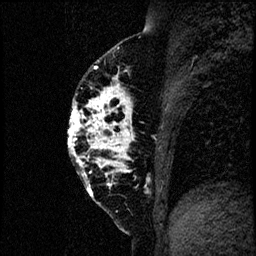
Breast MRI (dynamic contrast-enhanced), one sagittal slice. Slice 33 of 60 in the series (ordered by position). Dynamic contrast-enhanced study with each time point stored as its own series, time point 2 of 4 at this slice position (early post-contrast, ordered by acquisition time). 1.5 T. TE 4.2 ms, TR 17.6 ms. 256 × 256 image matrix, field of view 200 × 200 mm. Patient: female, 40 years. From the clinical record (not read from this slice): setting: breast cancer imaged before/during neoadjuvant chemotherapy; receptor status: HER2-positive.
Structures marked on this image (semi-automatically segmented with operator editing):
- analysis volume of interest (the breast-tissue region the enhancement analysis was run in; not a lesion): bounding box <66,55,185,206> (left, top, right, bottom; pixels)
- tumour enhancement mask (voxels above the 100 % enhancement threshold inside the analysis volume of interest): <67,66,130,189>